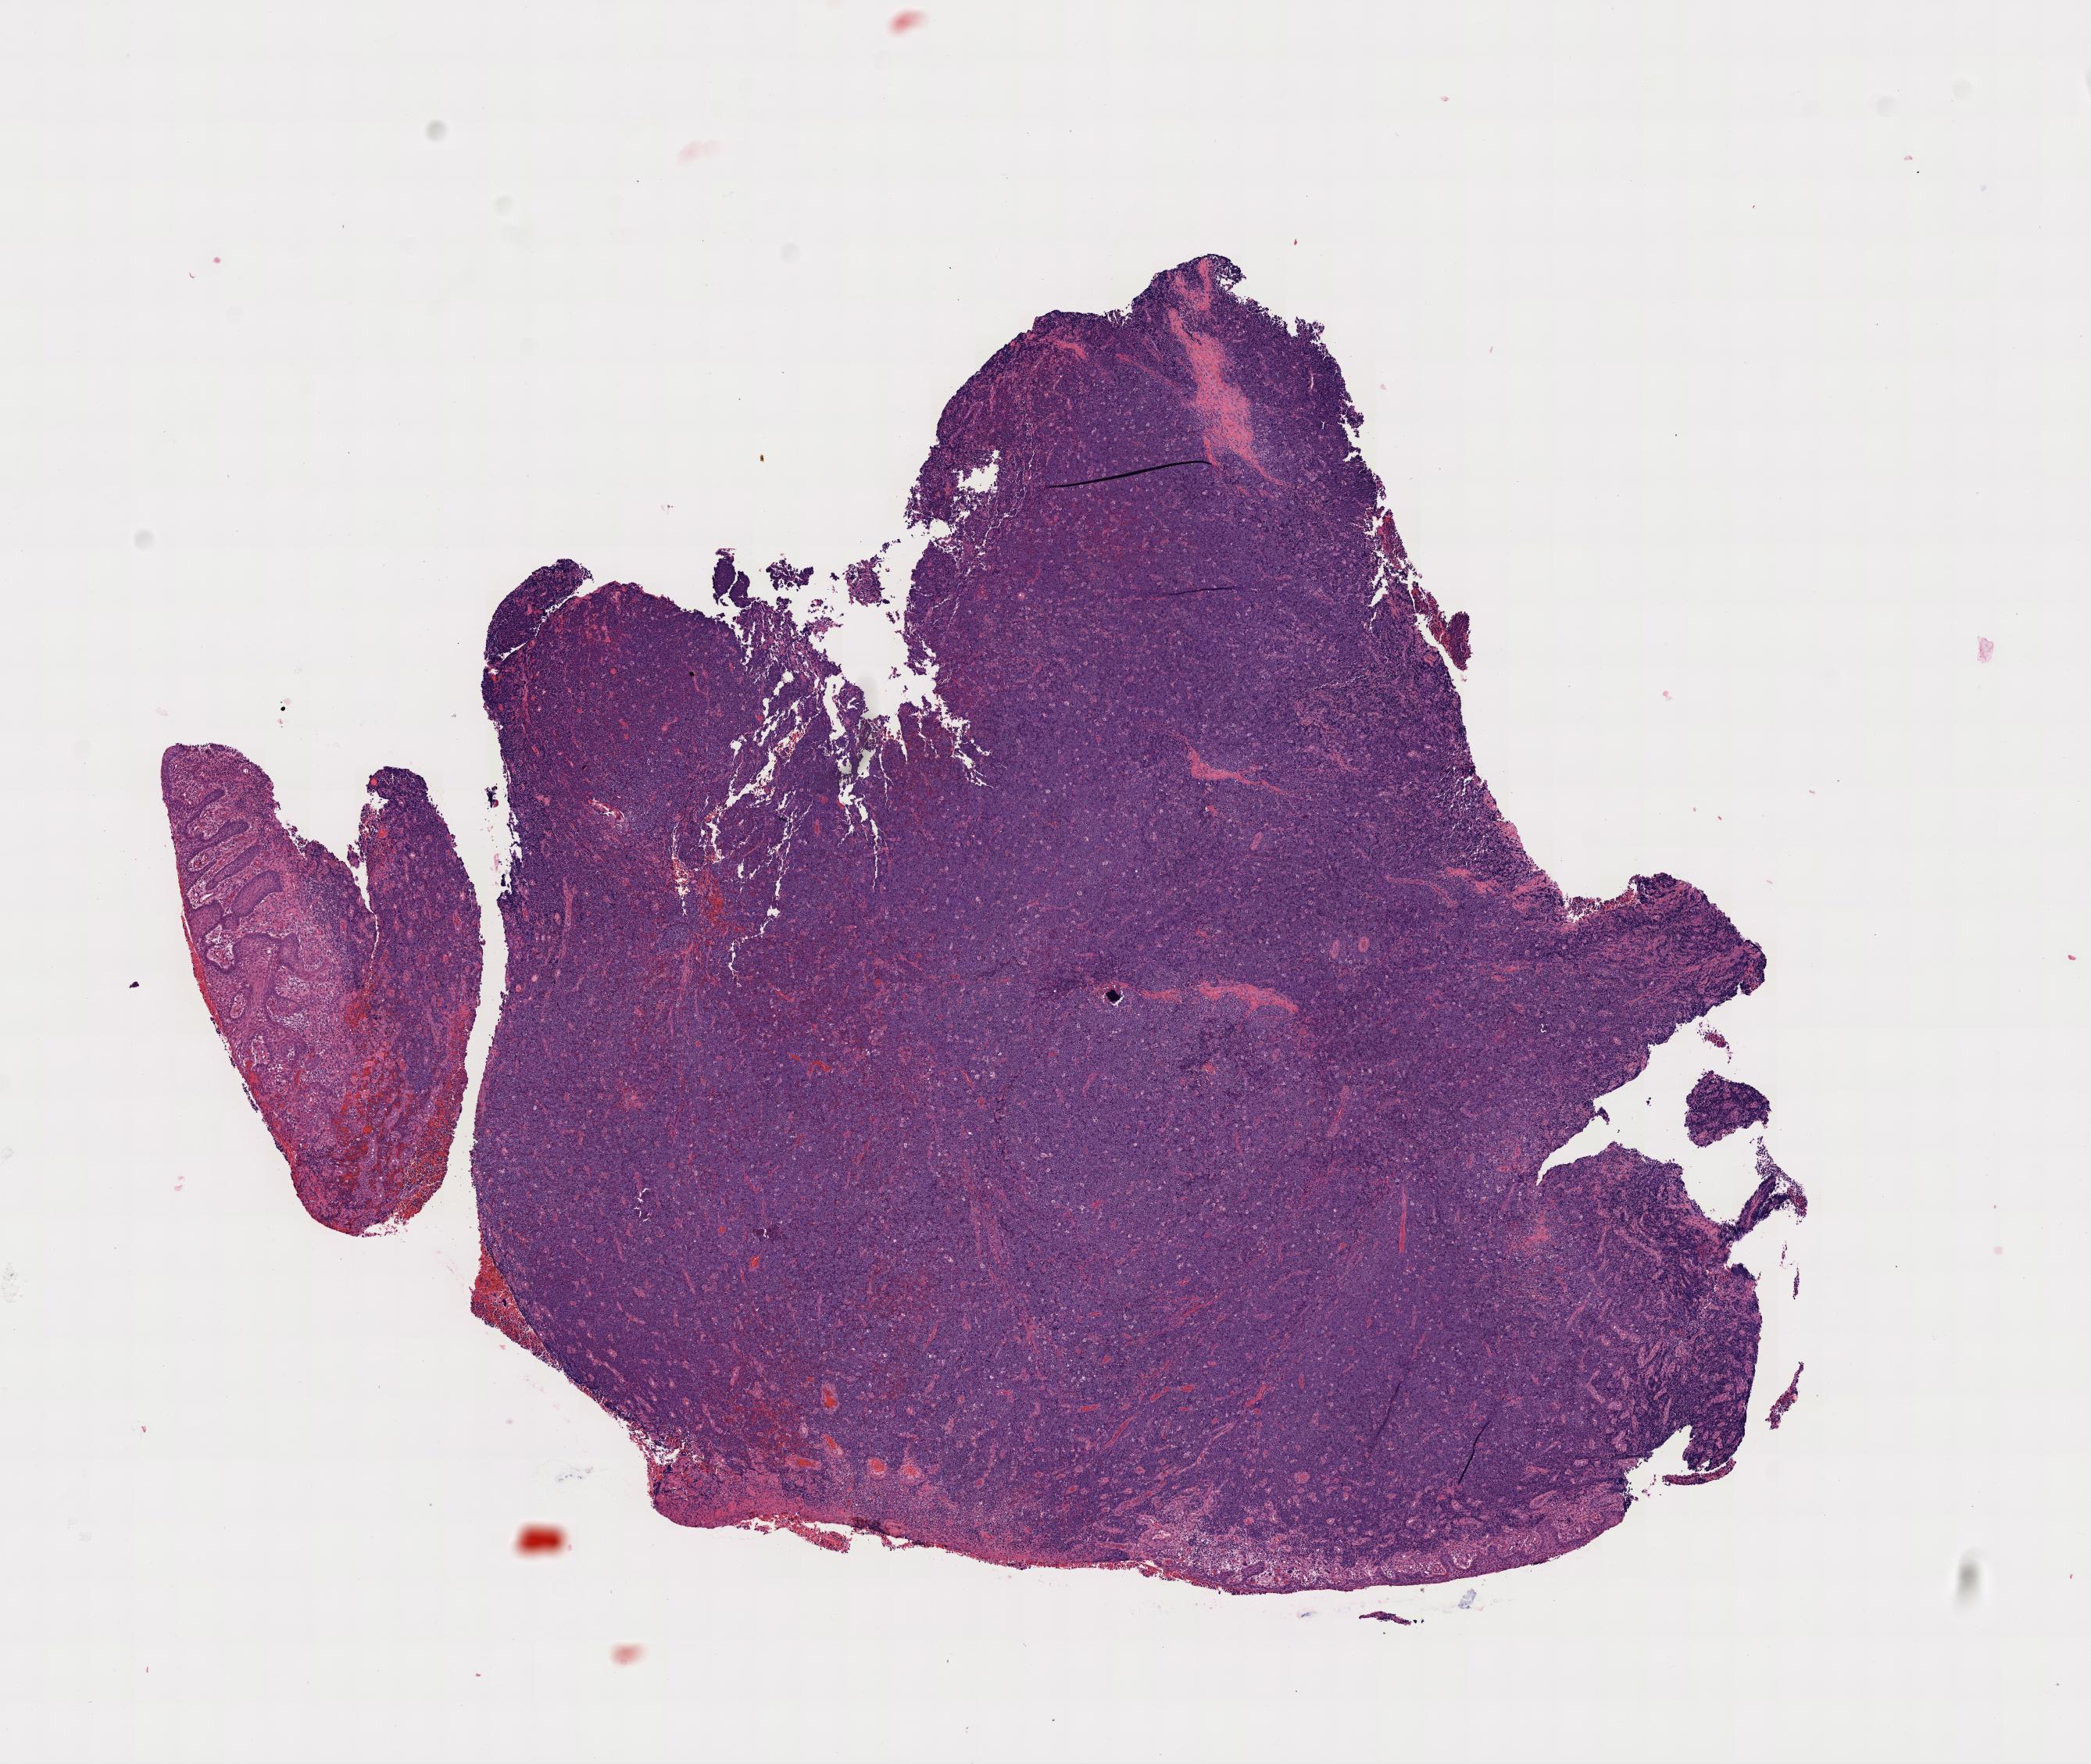
Digitized haematoxylin and eosin-stained section — low-resolution overview of the scanned area. Tumor tissue. Anatomic site: mandible. Male patient; age at initial diagnosis 4 years.
Histologic diagnosis: Burkitt lymphoma, NOS.